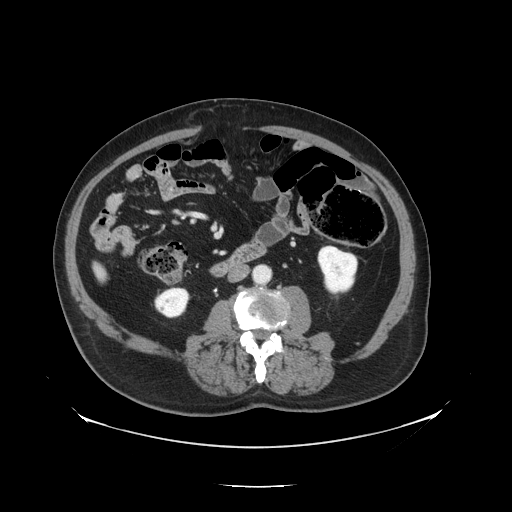
Contrast-enhanced abdominal CT, one axial slice; position 30 of 138 along the scan axis; 120 kVp; intravenous contrast given; soft-tissue window (W 400 / L 40 HU); 2.5 mm slice thickness; 512 × 512 image matrix, field of view 497 × 497 mm. Male patient, age 77 years. Case-level facts recorded for this patient, not image findings: diagnosis: colorectal cancer liver metastases, imaged before liver resection; multiple liver metastases: no; largest metastasis: 1.5 cm; disease in both lobes: no.
Outlined on this slice (manually delineated by an expert):
- liver: box from (x=95, y=265) to (x=108, y=281) px
- planned liver remnant (the part of the liver to remain after resection): (x=95, y=265)–(x=105, y=272)